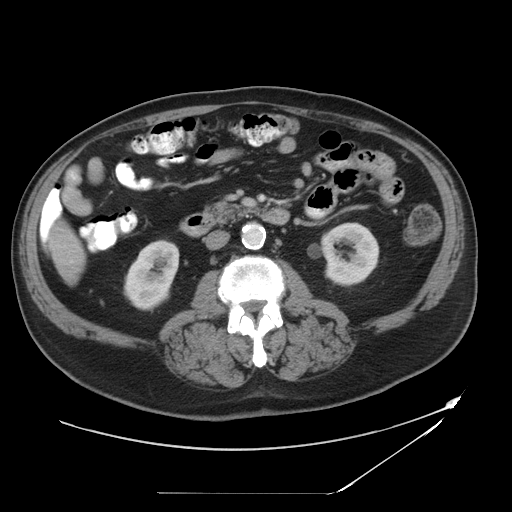
Contrast-enhanced abdominal CT, one axial slice; position 12 of 49 along the scan axis; reconstruction kernel STANDARD; 120 kVp; intravenous contrast given; soft-tissue window (W 400 / L 40 HU); 5 mm slice thickness; 512 × 512 image matrix. Male patient, age 72 years. Case-level facts recorded for this patient, not image findings: diagnosis: colorectal cancer liver metastases, imaged before liver resection; multiple liver metastases: no; largest metastasis: 2.5 cm; disease in both lobes: no.
Outlined on this slice (manually delineated by an expert):
- liver: bounding box [x1, y1, x2, y2] px = [52, 227, 84, 282]
- planned liver remnant (the part of the liver to remain after resection): [52, 227, 84, 282]